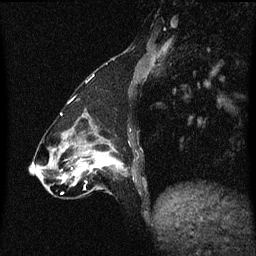
Breast MRI (dynamic contrast-enhanced), one sagittal slice. Slice 16 of 60 in the series (ordered by position). Dynamic contrast-enhanced series, image 2 of 3 at this slice position (ordered by acquisition). 1.5 T. TE 4.2 ms, TR 8.4 ms. 256 × 256 image matrix, field of view 200 × 200 mm. Patient: female, 47 years.
Structures marked on this image (semi-automatically segmented with operator editing):
- analysis volume of interest (the breast-tissue region the enhancement analysis was run in; not a lesion): bounding box [x1, y1, x2, y2] px = [81, 140, 133, 195]
- tumour enhancement mask (voxels above the 70 % enhancement threshold inside the analysis volume of interest): [81, 156, 120, 183]